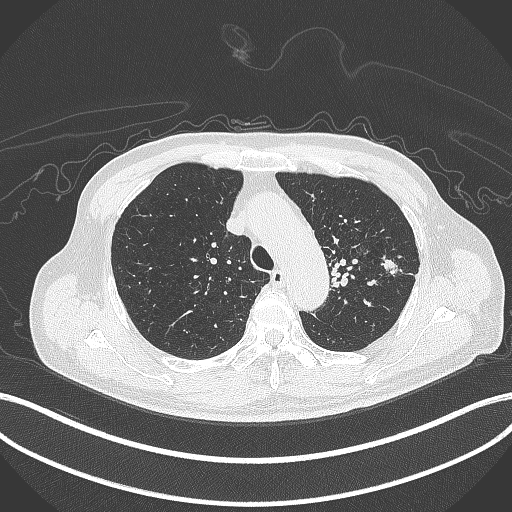
Chest CT, one axial slice; slice 331 of 417 in the series (ordered by position); reconstruction kernel B70f; 120 kVp; lung window (W 1500 / L -600 HU); 512 × 512 image matrix, field of view 400 × 400 mm. Patient: male, 77 years. From the clinical record (not read from this slice): clinical TNM (as recorded): T3 N1 M0.
Annotated regions visible in this slice (rectangle marked by the reading radiologist):
- lung tumour (recorded histology: adenocarcinoma): bounding box <380,254,401,278> (left, top, right, bottom; pixels)